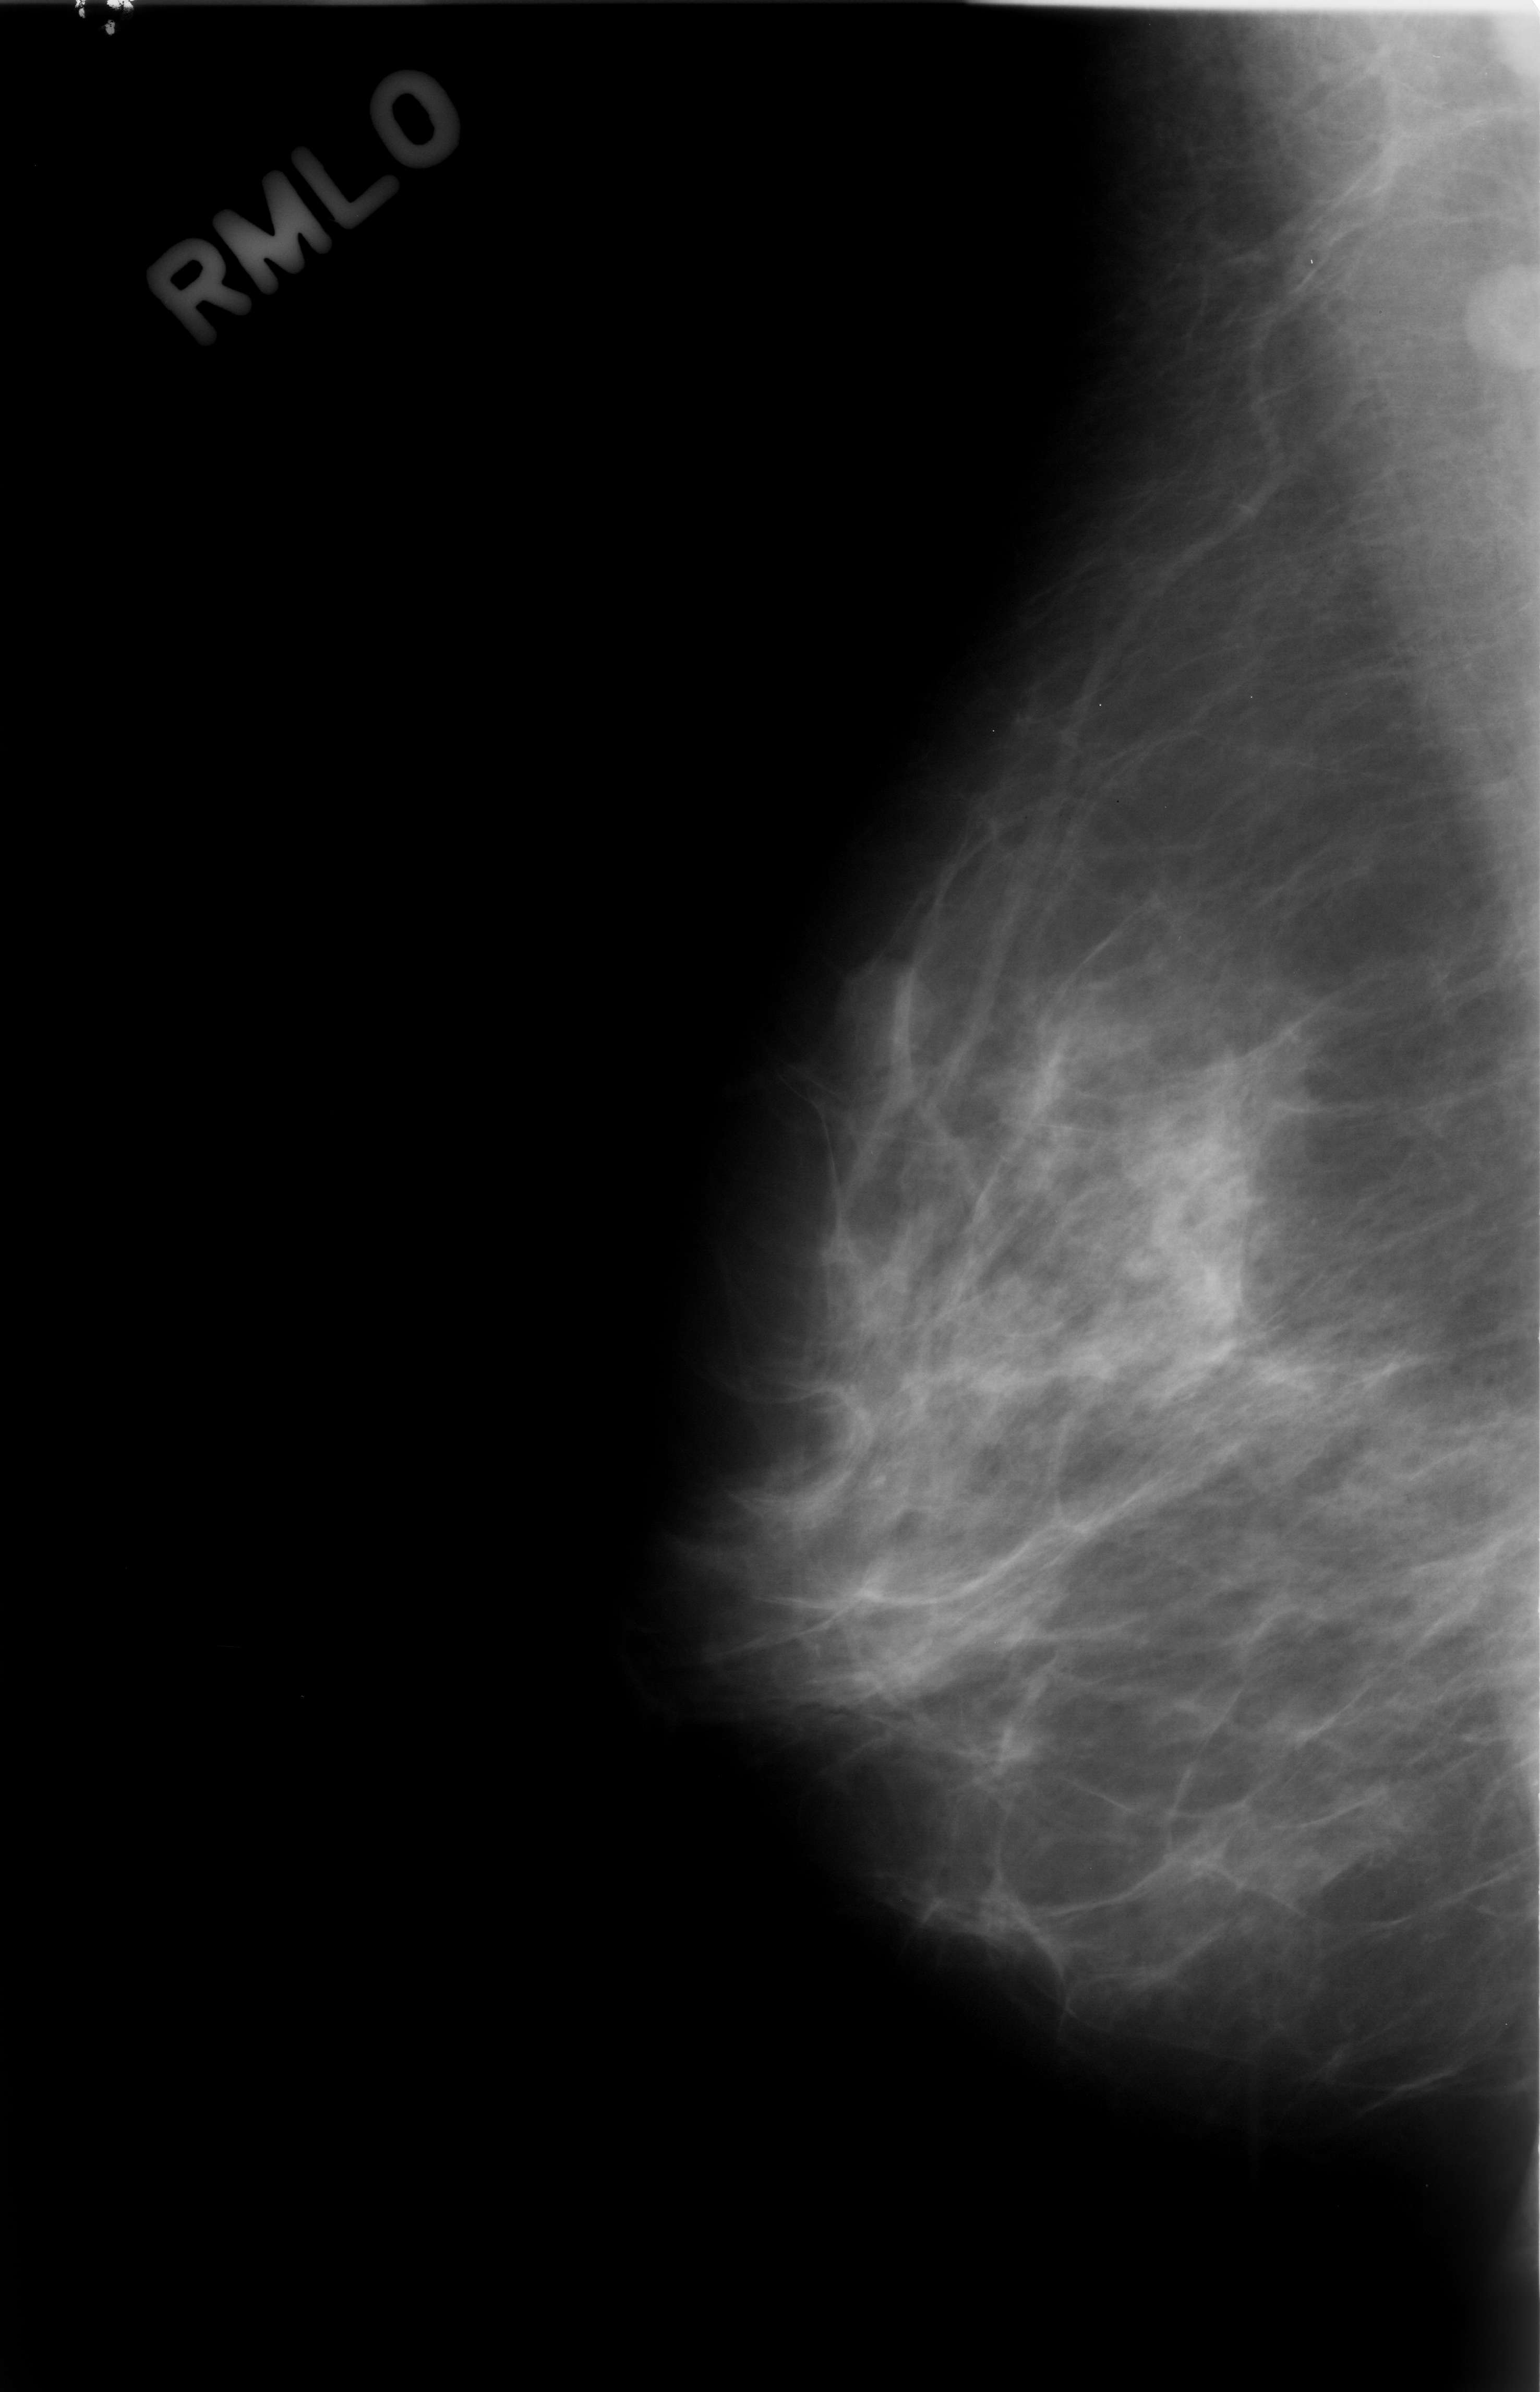
Mammogram (digitized film); right breast; mediolateral oblique (MLO) view.
Radiologist-marked abnormalities on this image: mass, shape round, margins circumscribed; BI-RADS assessment category 3; benign without callback (not worked up further).